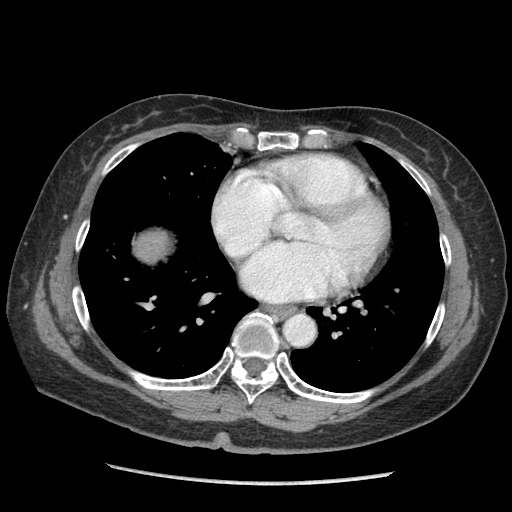
Contrast-enhanced abdominal CT (liver protocol), one axial slice; slice 99 of 105 in the series (ordered by position); reconstruction kernel STANDARD; soft-tissue window (W 400 / L 40 HU); 2.5 mm slice thickness; 512 × 512 image matrix. From the clinical record (not read from this slice): diagnosis: hepatocellular carcinoma (patient treated with transarterial chemoembolisation; whether this scan precedes or follows treatment is not stated here); TNM stage (as recorded): Stage-I; Child-Pugh class: A; tumour nodularity: uninodular; tumour size: 11.1 cm.
Annotated regions visible in this slice (semi-automatic segmentation, software-assisted and operator-edited):
- liver parenchyma outside the tumour (the mass and vessels are separate outlines, so this box may not span the whole liver): bounding box [x1, y1, x2, y2] px = [136, 232, 166, 259]